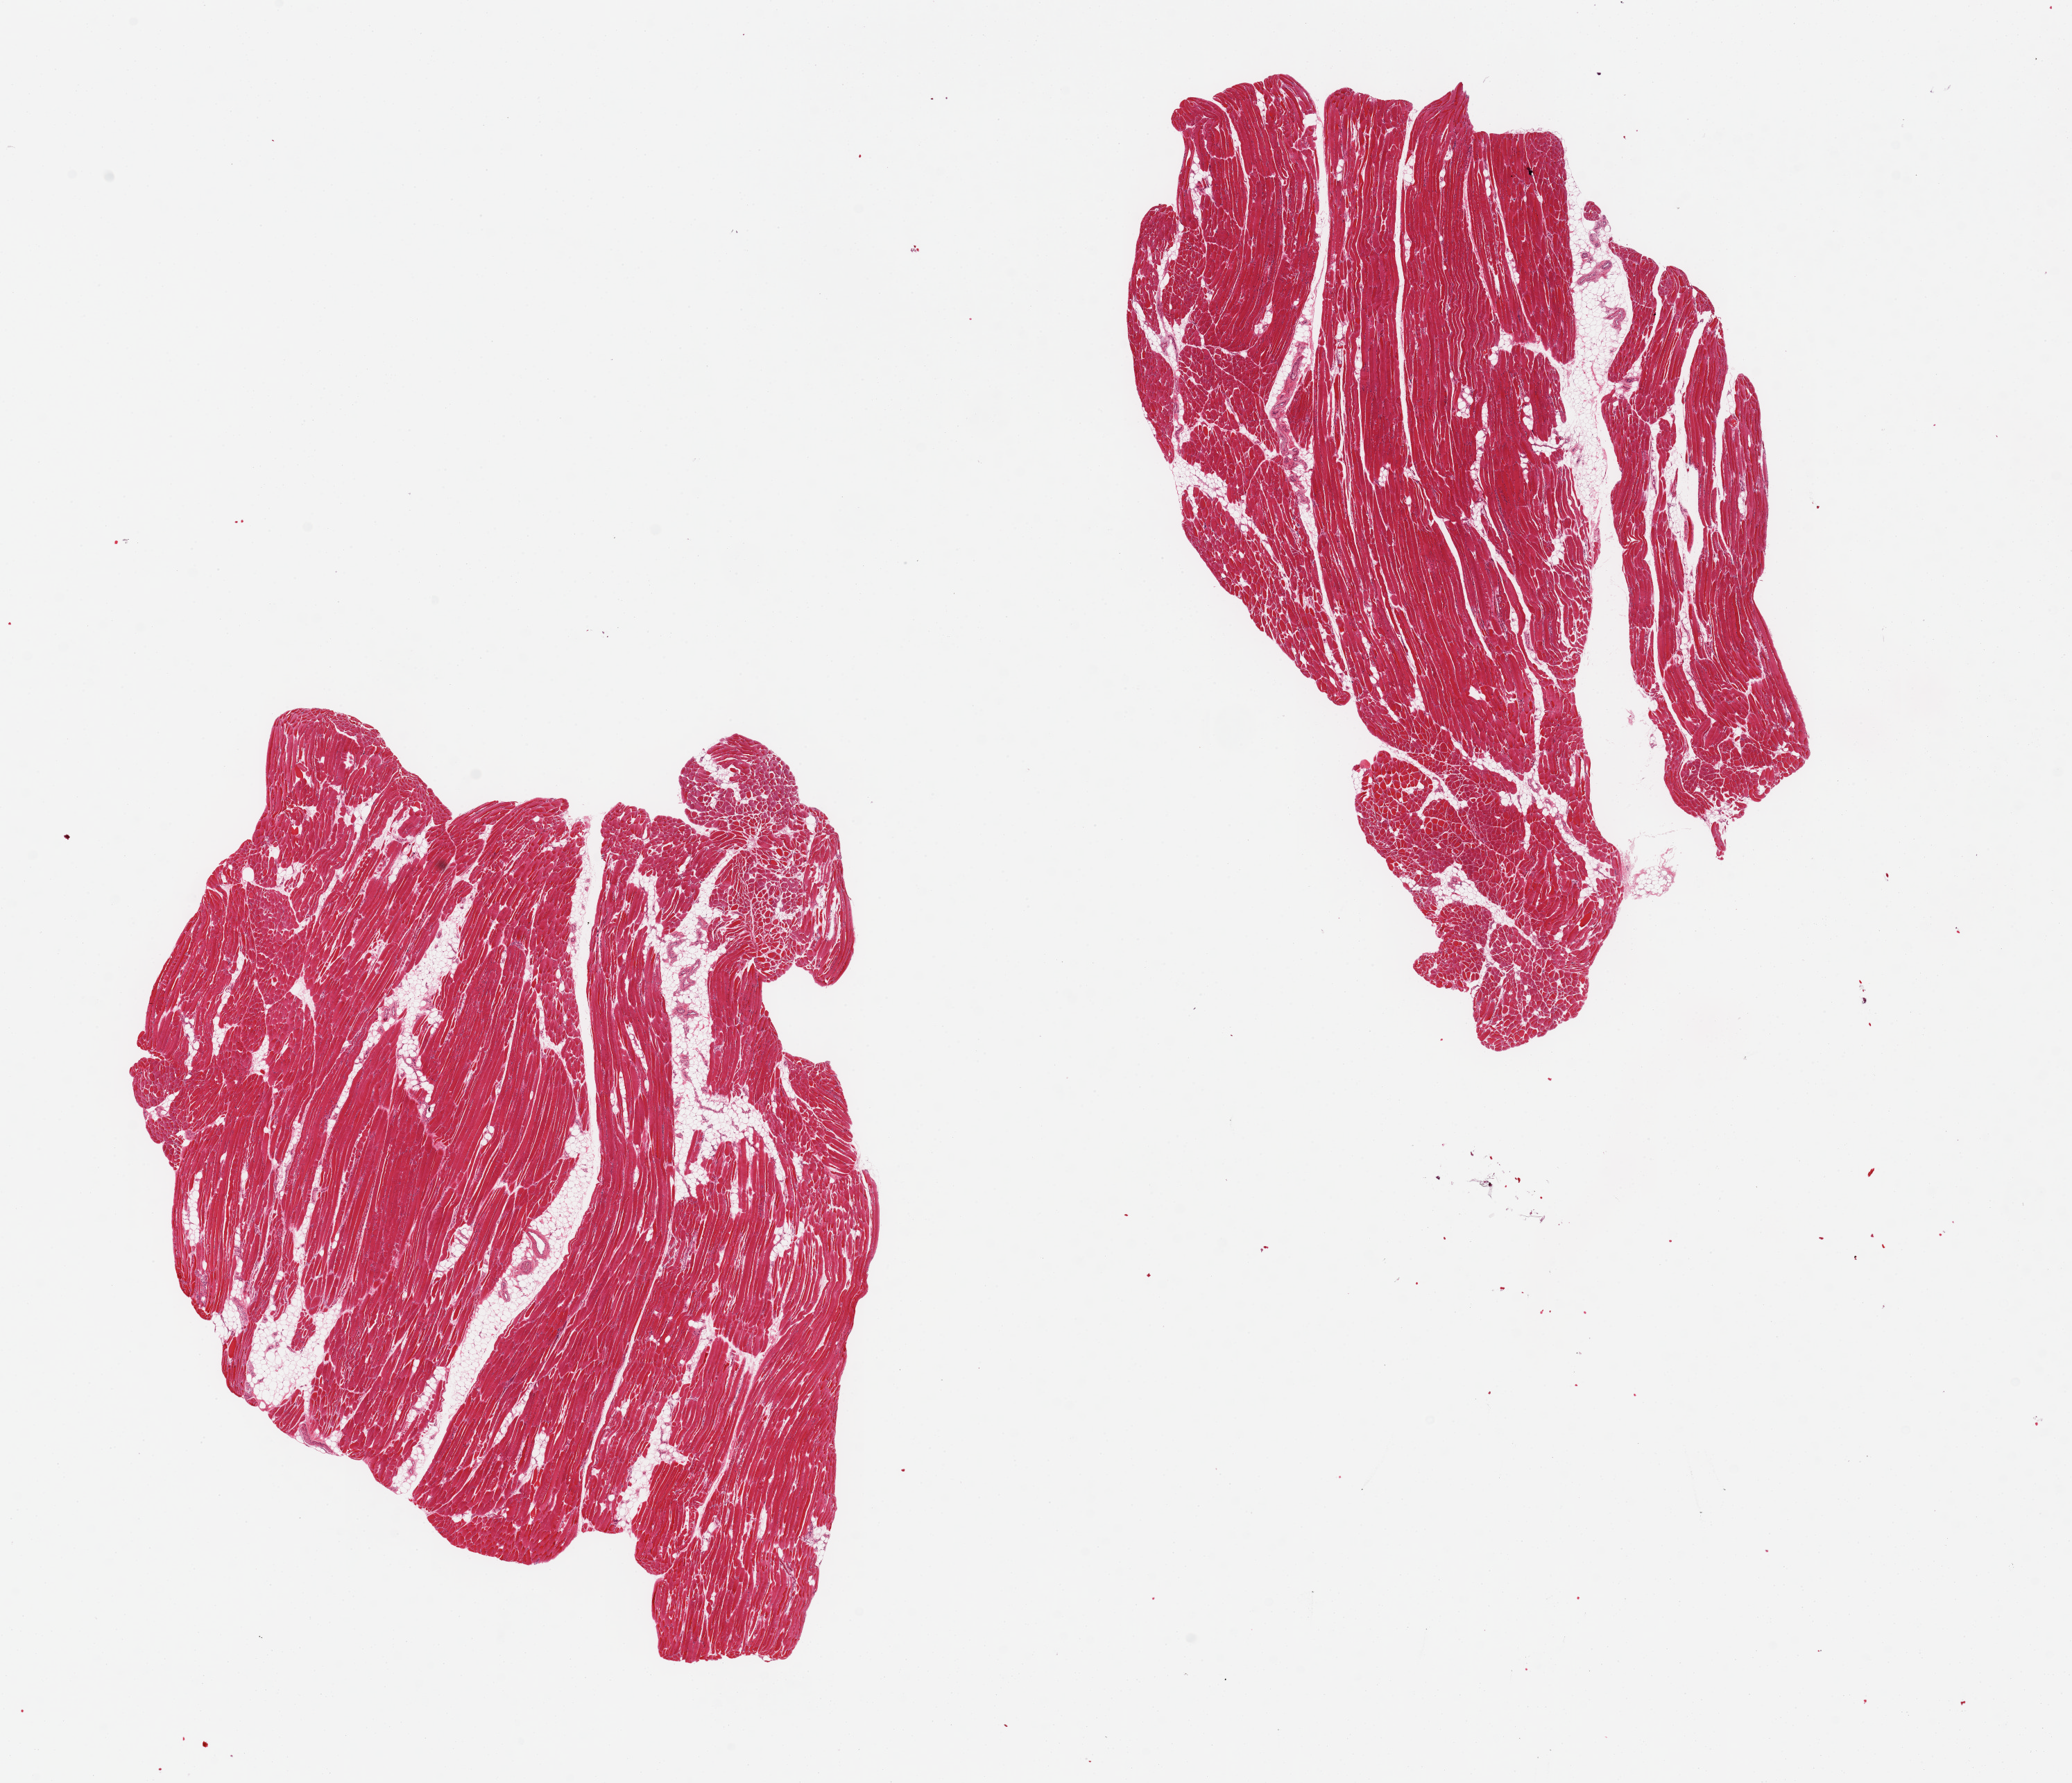
Digitized haematoxylin and eosin-stained section, brightfield — a low-resolution overview of the entire scanned area, about 23.6 x 20.3 mm (slide scanned at 20x); PAXgene-fixed paraffin-embedded (PFPE) section; target tissue: skeletal muscle; donor tissue sample. Female donor.
Pathologist's review note for this sample: 2 pieces, 10-15% interstitial fat, foci deineated.